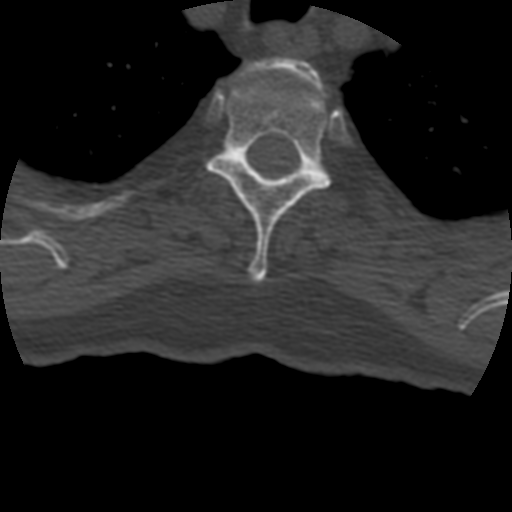
CT including the spine, one axial slice; slice 353 of 399 in the series (ordered by position); reconstruction kernel STANDARD; 120 kVp; bone window (W 1800 / L 400 HU); 1.25 mm slice thickness; 512 × 512 image matrix, field of view 160 × 160 mm. Patient age 69 years. Case-level facts recorded for this patient, not image findings: primary cancer: prostate.
Annotated regions visible in this slice (semi-automatic segmentation, software-assisted and operator-edited):
- T2 vertebra: bounding box (x1, y1, x2, y2) in pixels: (251, 58, 321, 85)
- T3 vertebra: (207, 78, 331, 282)